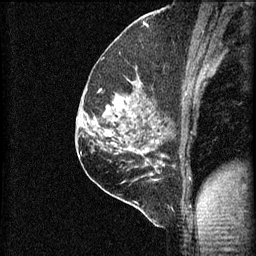
Breast MRI (dynamic contrast-enhanced), one sagittal slice; slice 39 of 60 in the series (ordered by position); 3 images stored at this slice position (order not interpretable as contrast timing); 1.5 T; TE 4.2 ms, TR 8.2 ms; 256 × 256 image matrix. Female patient, age 59 years.
Annotated regions visible in this slice (semi-automatically segmented with operator editing):
- analysis volume of interest (the breast-tissue region the enhancement analysis was run in; not a lesion): bounding box [x1, y1, x2, y2] px = [92, 76, 155, 131]
- tumour enhancement mask (voxels above the 70 % enhancement threshold inside the analysis volume of interest): [107, 98, 123, 115]